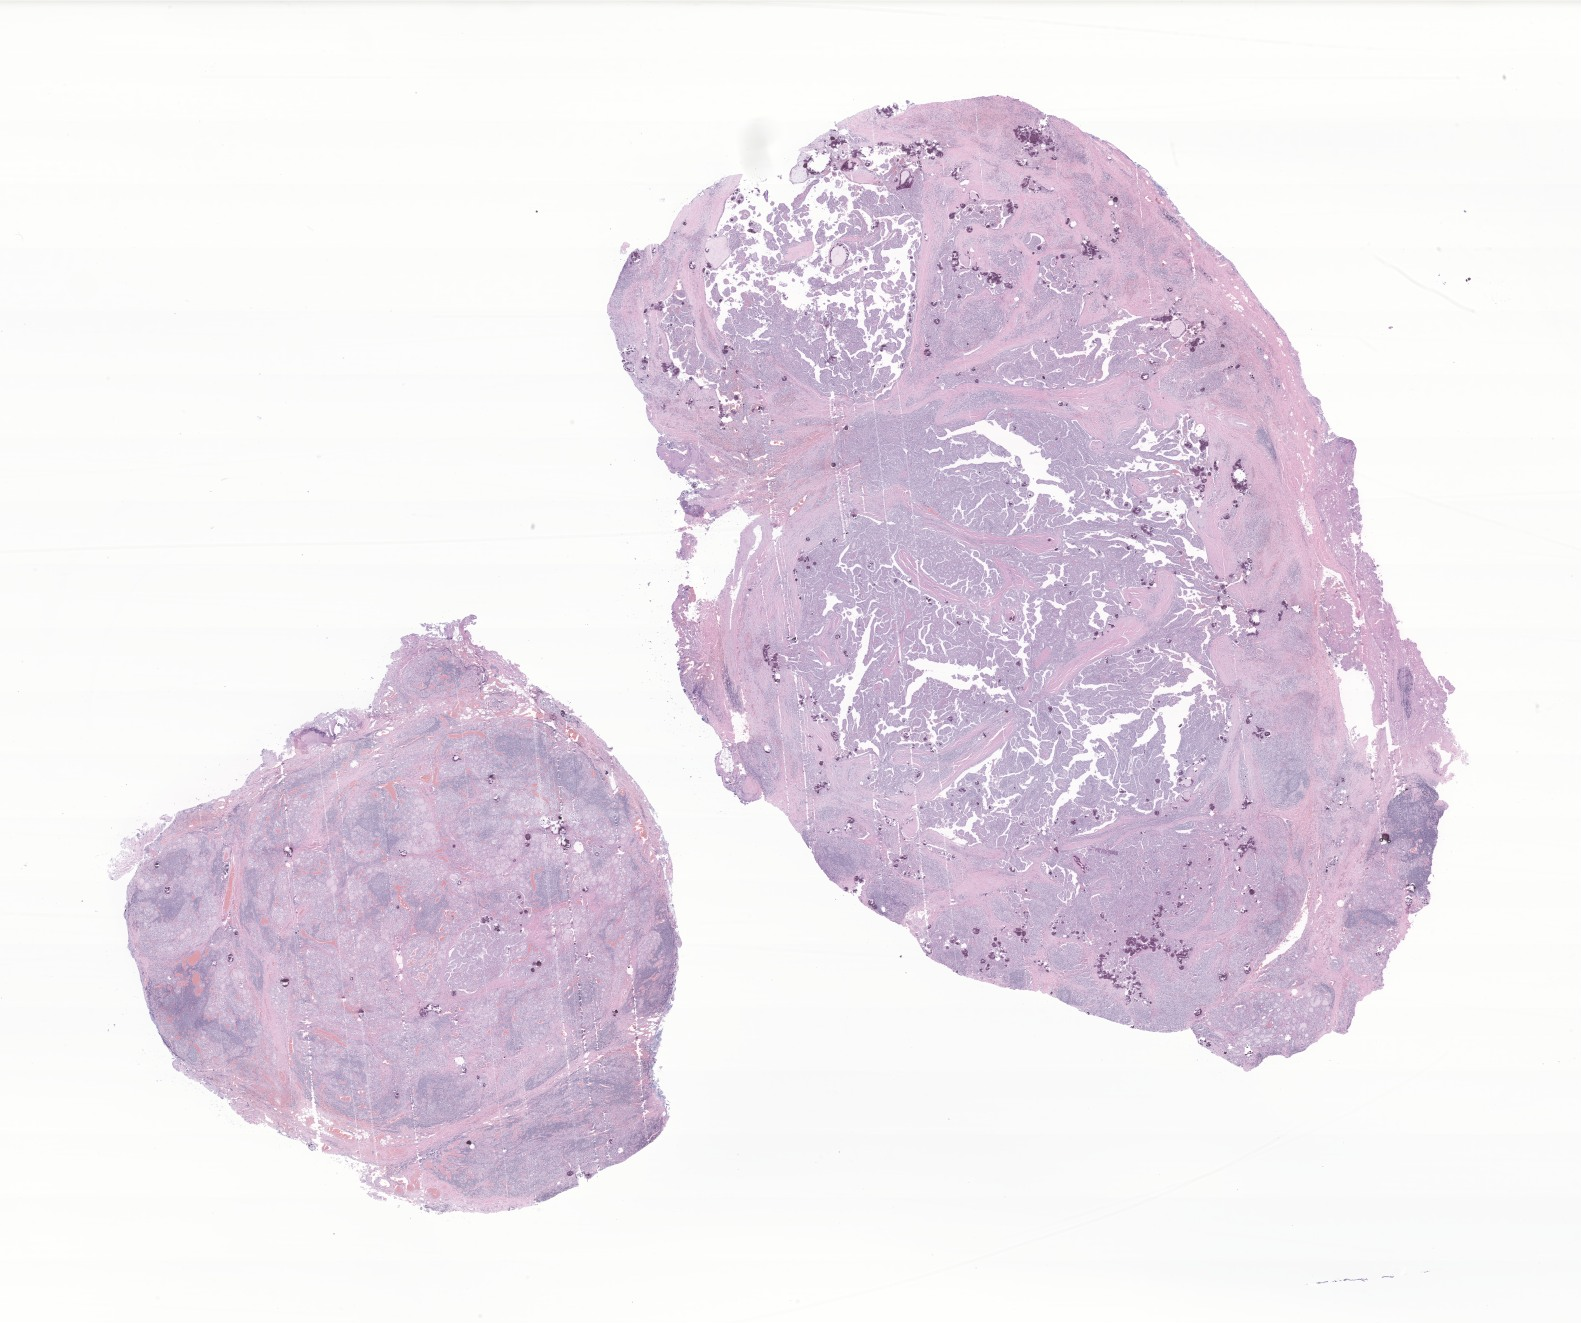
Digitized hematoxylin and eosin (H&E)-stained section of tumor tissue from the thyroid — shown as a low-resolution overview of the whole scanned area (about 26.7 x 22.3 mm); formalin-fixed, paraffin-embedded (FFPE) tissue. Female patient, age 136 months (11 years 4 months).
Recorded diagnosis: Papillary carcinoma, NOS.